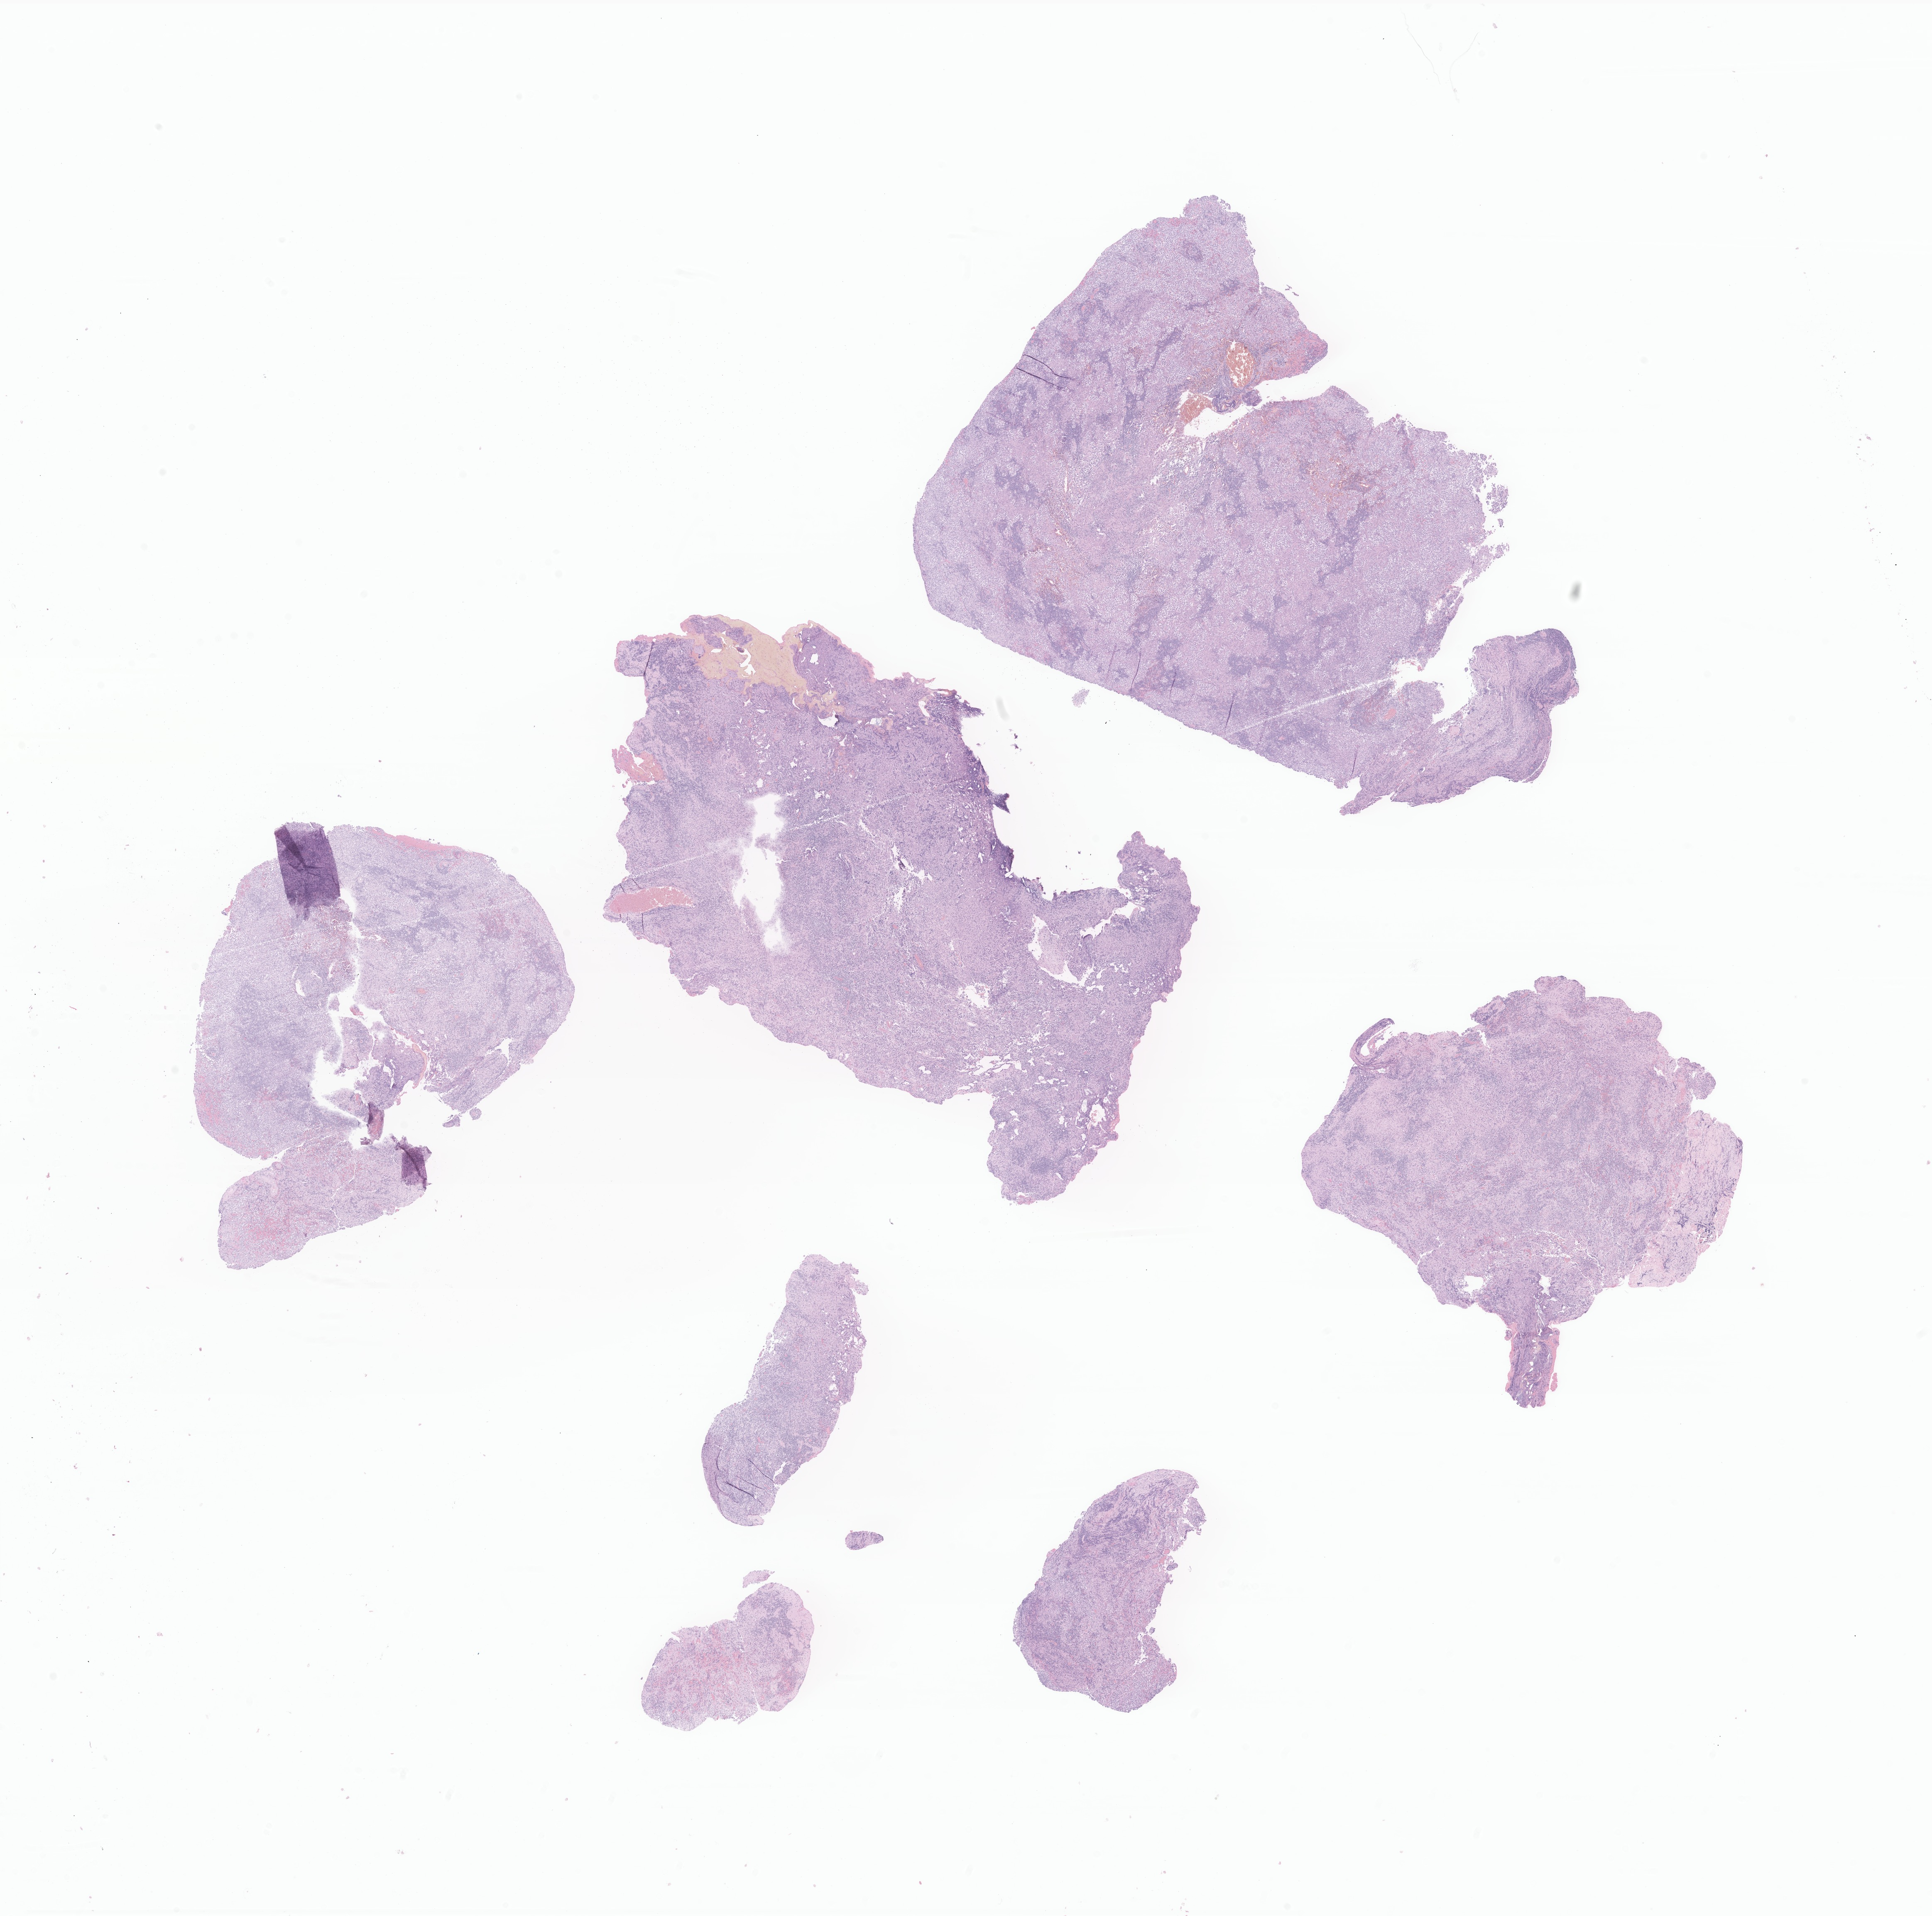
Digitized H&E-stained section of tumor tissue from the brain — low-resolution overview of the scanned area, about 19.6 x 19.4 mm, formalin-fixed paraffin-embedded section. Patient: male, age 240 months (20 years).
Diagnosis: Dysgerminoma.